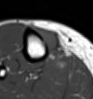
MRI of an extremity soft-tissue mass, one axial slice; position 20 of 54 along the scan axis; MR volume resampled by the dataset authors to the PET/CT grid (not the native acquisition matrix); 3.27 mm slice thickness; 93 × 99 image matrix. Female patient. Case-level facts recorded for this patient, not image findings: histological type: undifferentiated – high grade; grade: high; site of the primary tumour: right thigh.
Structures marked on this image (expert contour drawn on MRI and transferred to this co-registered scan by the dataset authors):
- gross tumour volume (mass): box from (x=36, y=27) to (x=60, y=58) px